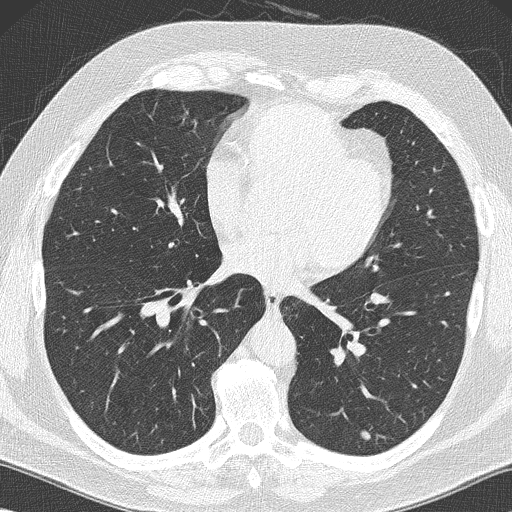
Chest CT (low-dose screening protocol), one axial image; baseline screening round; lung window (W 1500 / L -600 HU); 2 mm slice thickness; slice 92 of 152 in the series. Male participant, aged 59 years at enrolment. Former smoker at enrolment.
Lesion marked by an expert reader, bounding box <343,418,384,453> (left, top, right, bottom; pixels). The screening reader recorded 2 non-calcified nodules or masses ≥4 mm on this exam (left lower lobe, left lower lobe); which of them this box marks is not recorded. Later outcome: lung cancer diagnosed 61 days after this screen — large cell carcinoma, NOS, left lower lobe, poorly differentiated (G3), stage IA (AJCC 6th edition), 14 mm at pathology.